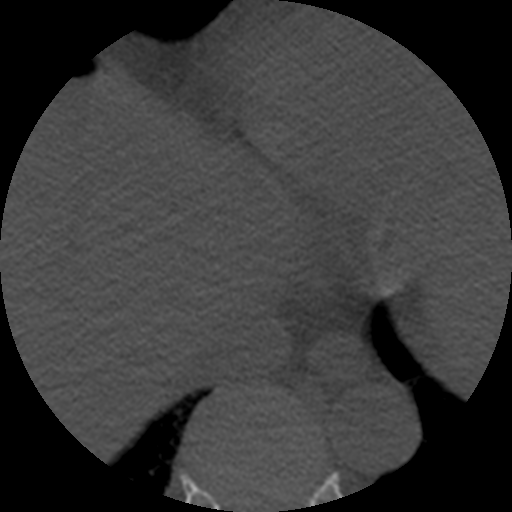
CT including the spine, one axial slice. Position 300 of 508 along the scan axis. Bone window (W 1800 / L 400 HU). 1.25 mm slice thickness. 512 × 512 image matrix, field of view 160 × 160 mm. Patient age 57 years. Case-level facts recorded for this patient, not image findings: primary cancer: prostate.
Structures marked on this image (semi-automatically segmented with operator editing):
- T8 vertebra: bounding box <220,497,276,509> (left, top, right, bottom; pixels)
- T9 vertebra: <278,488,308,502>